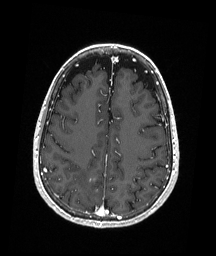
Brain MRI from a brain-tumour surgery series, one axial slice; position 73 of 192 along the scan axis; T1-weighted post-contrast; 1 mm slice thickness; 216 × 256 image matrix, field of view 211 × 250 mm. Case-level facts recorded for this patient, not image findings: histopathology: Astrocytoma; WHO grade: 3; IDH mutation: yes; tumour location: Right Parietal.
Structures marked on this image (outlined manually by an expert reader):
- tumour: bounding box (x1, y1, x2, y2) in pixels: (88, 177, 99, 193)